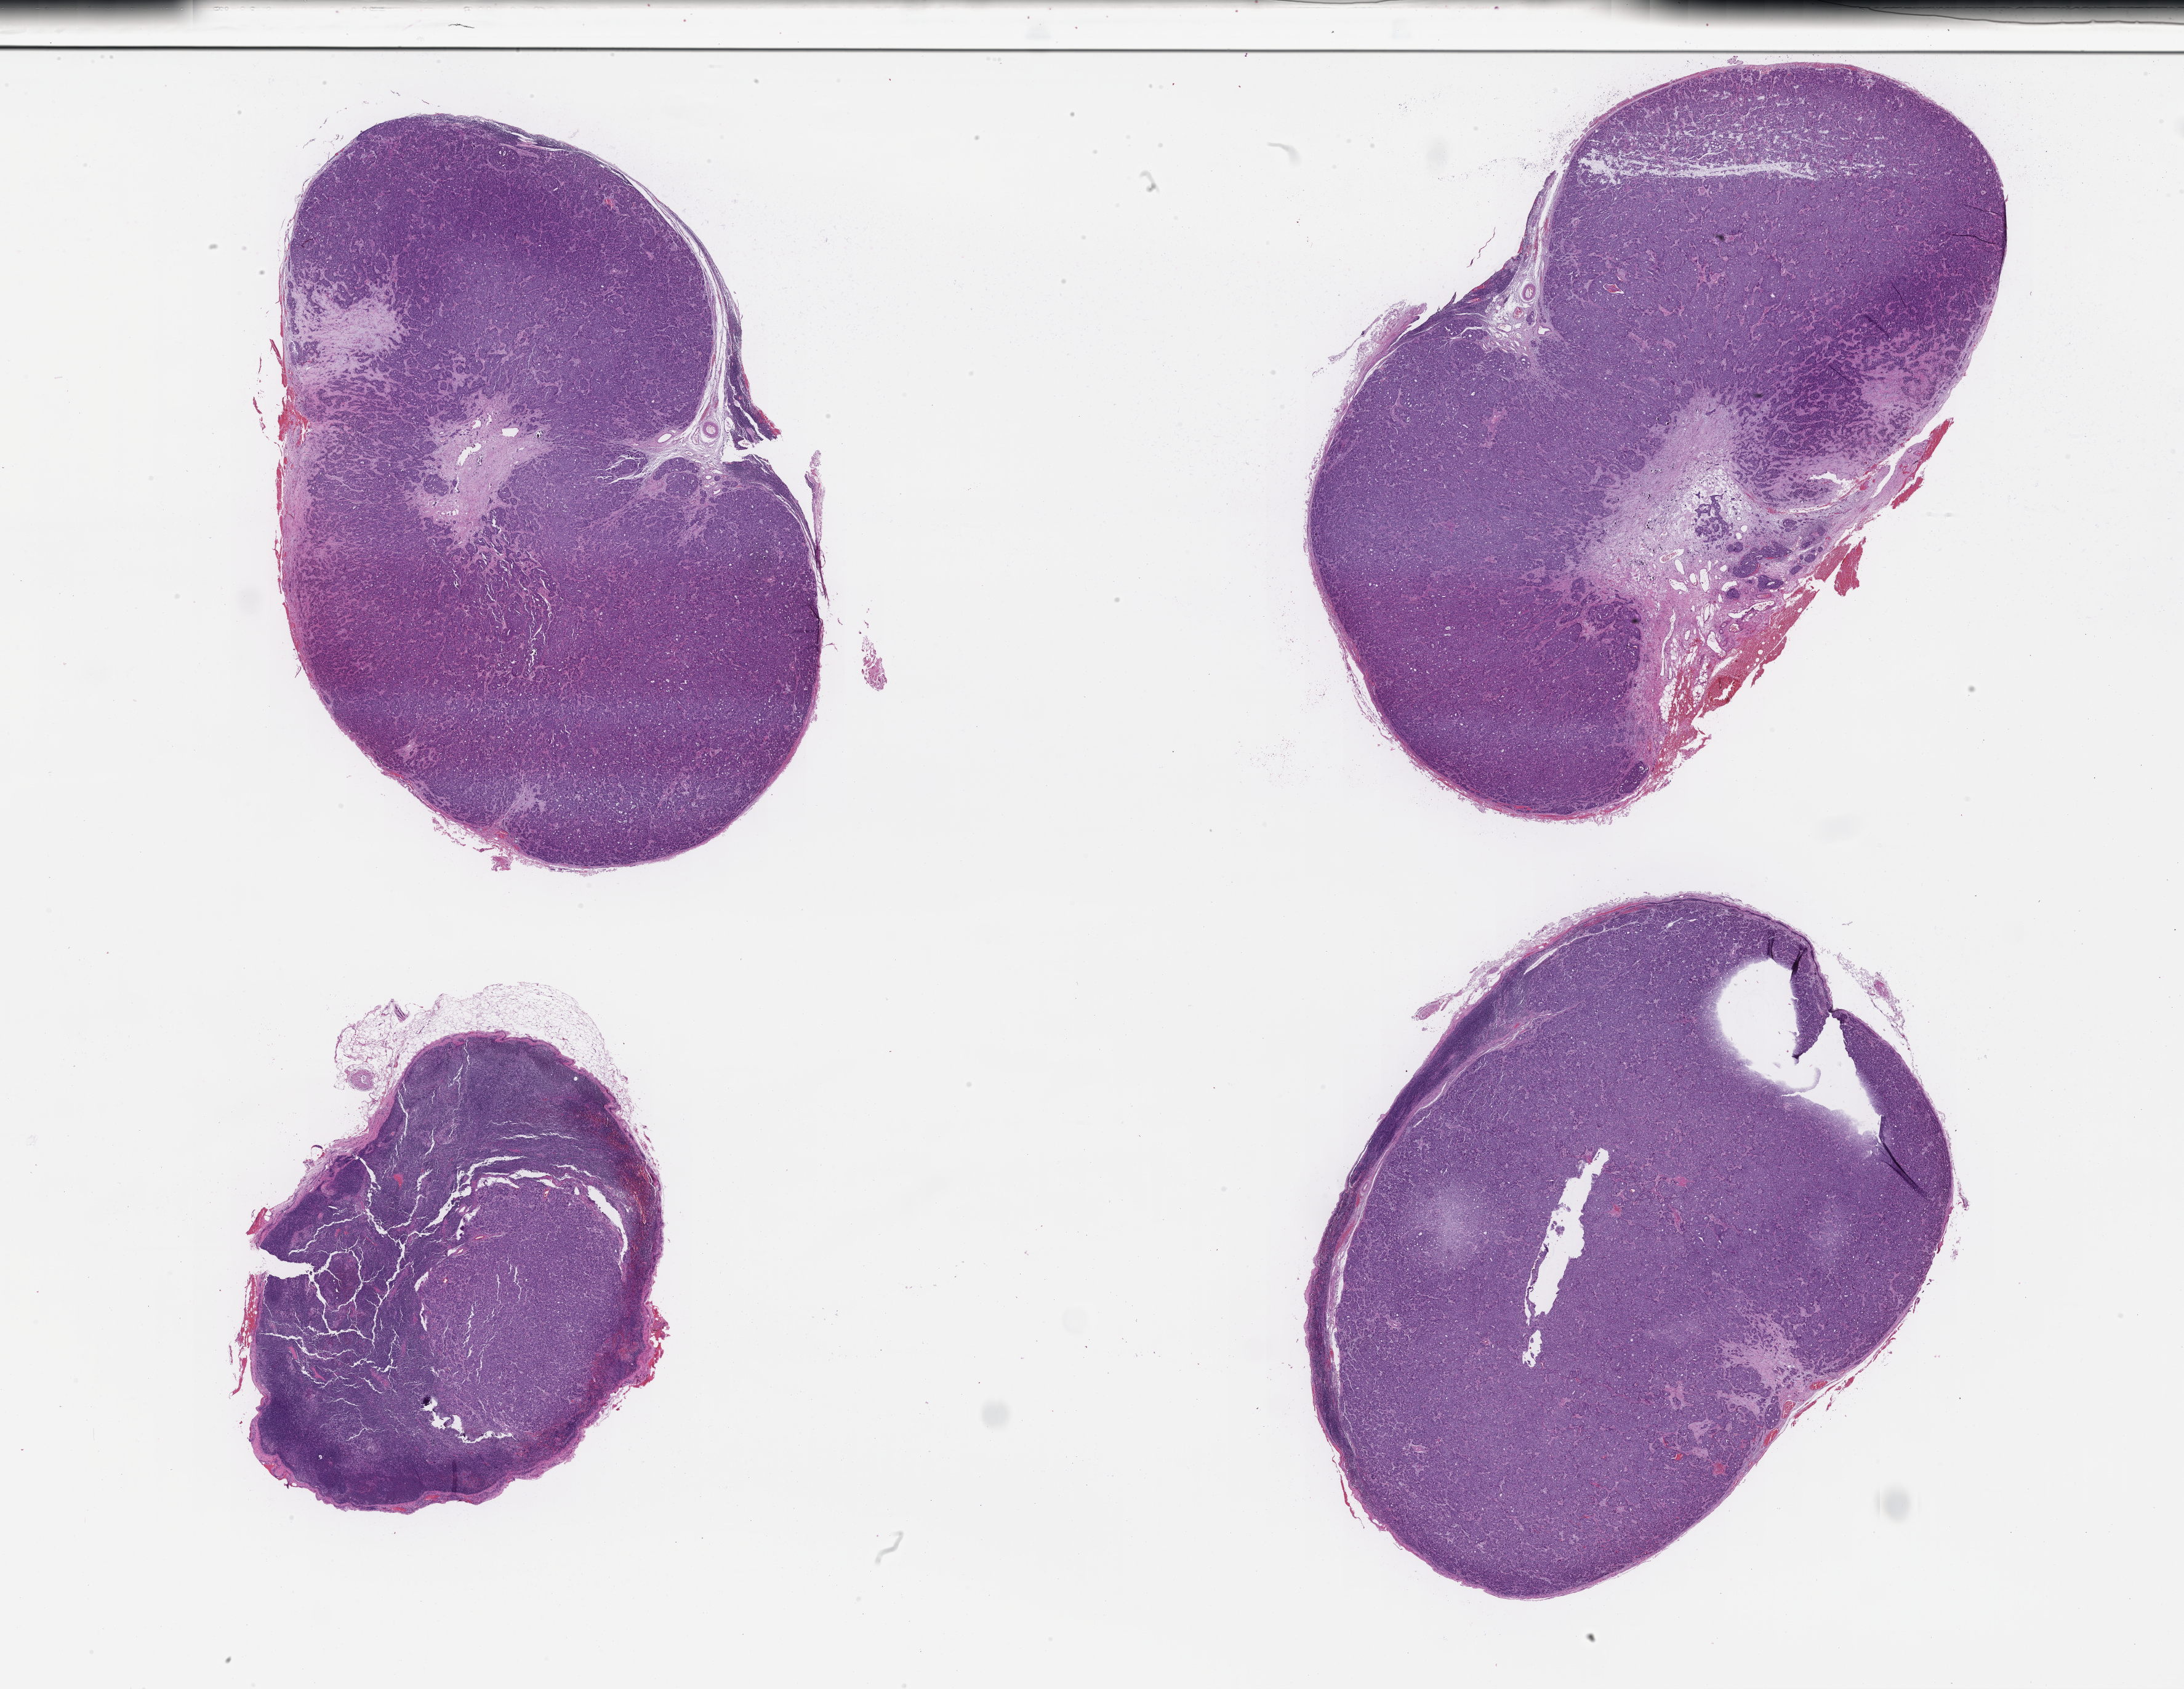
Whole-slide image, haematoxylin and eosin stain — shown as a low-resolution overview of the whole scanned area (about 28.6 x 22.2 mm); formalin-fixed paraffin-embedded section; specimen time point: archival tissue. Patient: female.
• this section: metastasis (sampled organ not recorded)
• patient diagnosis (primary): Invasive Breast Carcinoma